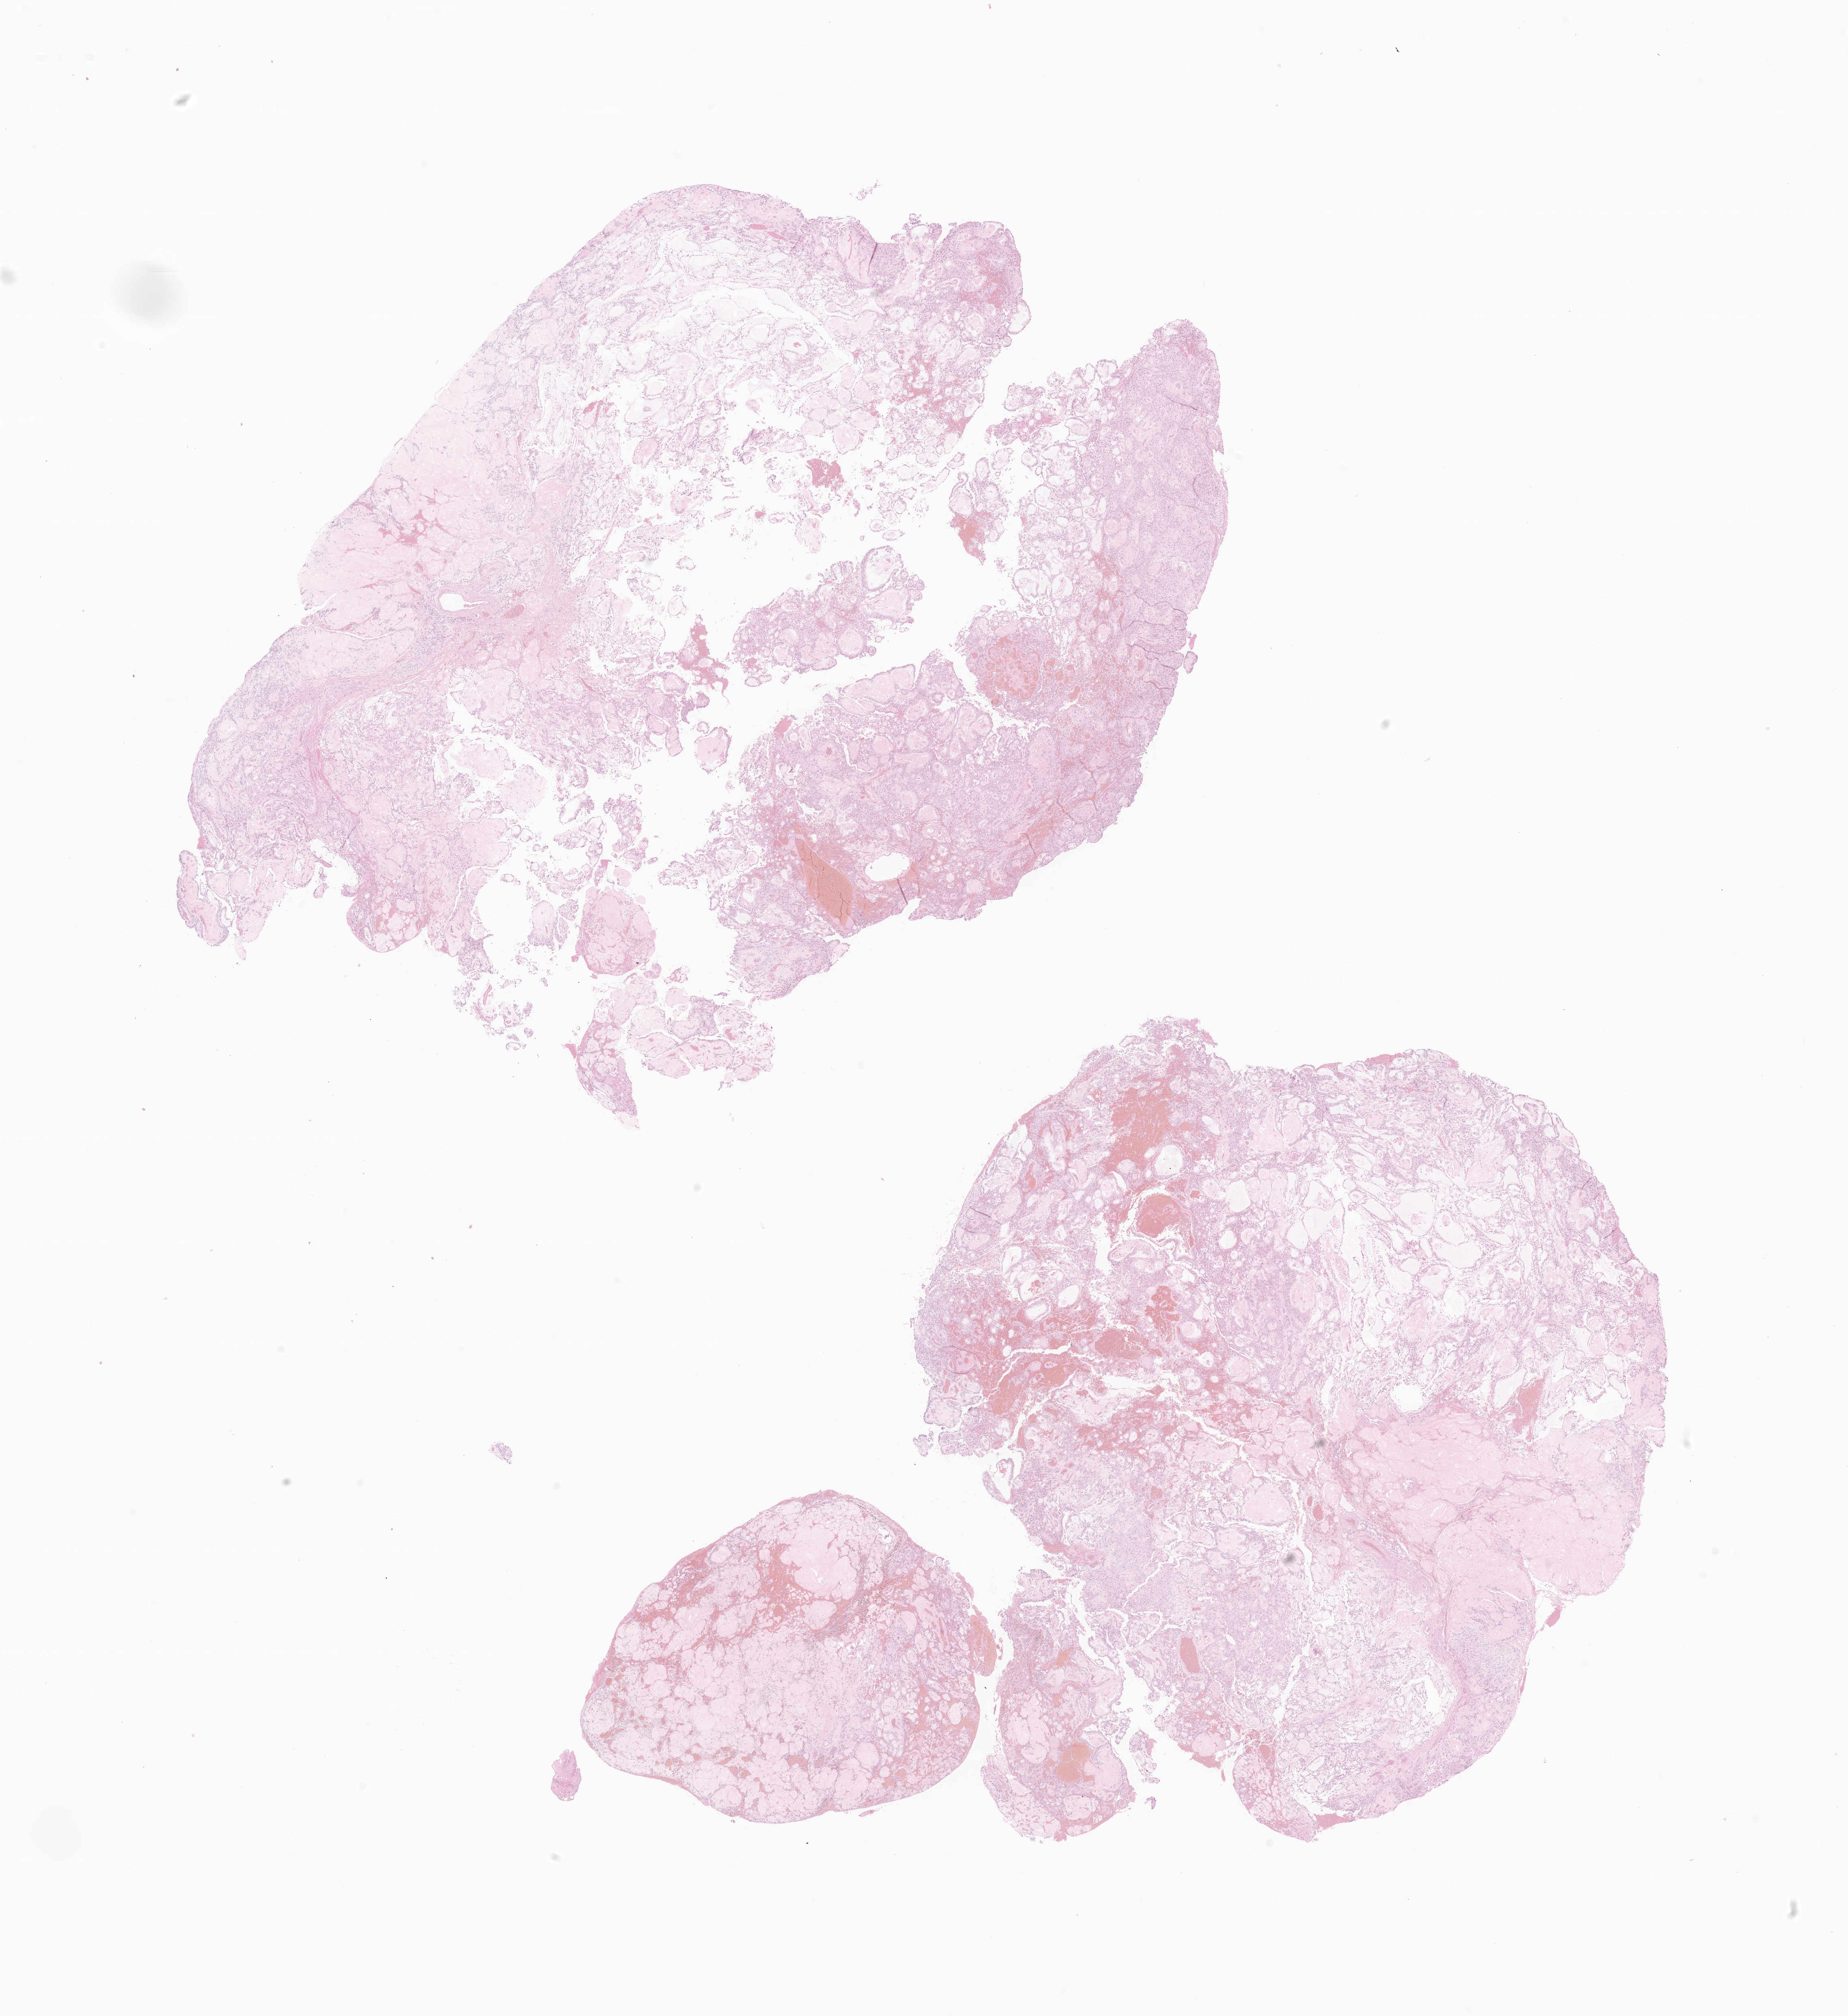
Digitized H&E-stained section of tumor tissue from the spinal cord — shown as a low-resolution overview of the whole scanned area (about 19.2 x 20.9 mm), FFPE section. Male patient, age 233 months (19 years 5 months).
Diagnosis: Myxopapillary ependymoma.